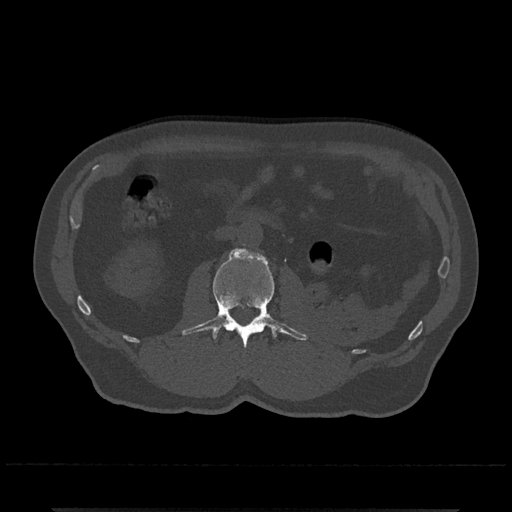
CT including the spine, one axial slice. Position 291 of 797 along the scan axis. Bone window (W 1800 / L 400 HU). 0.5 mm slice thickness. 512 × 512 image matrix, field of view 393 × 393 mm. Patient: male, 67 years. From the clinical record (not read from this slice): primary cancer: prostate.
Annotated regions visible in this slice (semi-automatic segmentation, software-assisted and operator-edited):
- L2 vertebra: bounding box (x1, y1, x2, y2) in pixels: (182, 248, 308, 348)